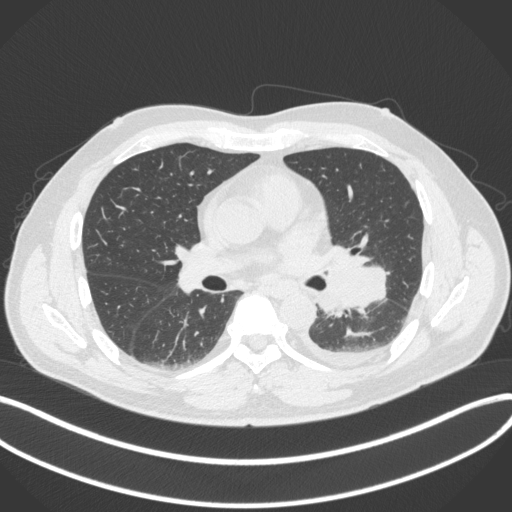
Chest CT, one axial slice. Slice 194 of 350 in the series (ordered by position). Reconstruction kernel B31f. Lung window (W 1500 / L -600 HU). 1 mm slice thickness. 512 × 512 image matrix. Male patient, age 58 years. From the clinical record (not read from this slice): clinical TNM (as recorded): T3 N1 M1b; histopathological grade: G3.
Structures marked on this image (rectangle marked by the reading radiologist):
- lung tumour (recorded histology: small cell carcinoma): bounding box [x1, y1, x2, y2] px = [315, 253, 388, 318]